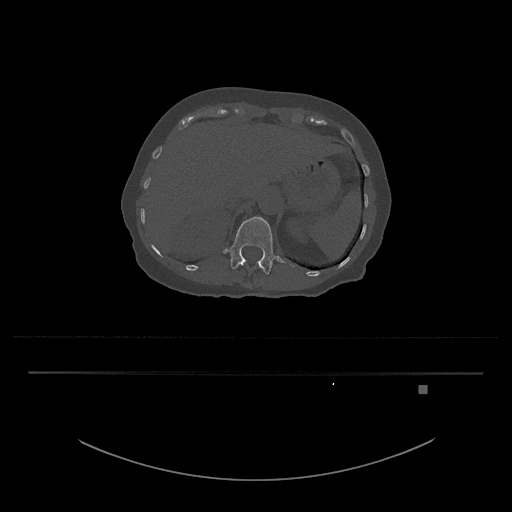
CT including the spine, one axial slice. Position 567 of 797 along the scan axis. 120 kVp. Bone window (W 1800 / L 400 HU). 0.5 mm slice thickness. 512 × 512 image matrix, field of view 500 × 500 mm. Female patient, age 57 years. Case-level facts recorded for this patient, not image findings: primary cancer: cervical.
Annotated regions visible in this slice (semi-automatically segmented with operator editing):
- L1 vertebra: bounding box (x1, y1, x2, y2) in pixels: (223, 217, 294, 274)
- T12 vertebra: (243, 262, 263, 270)